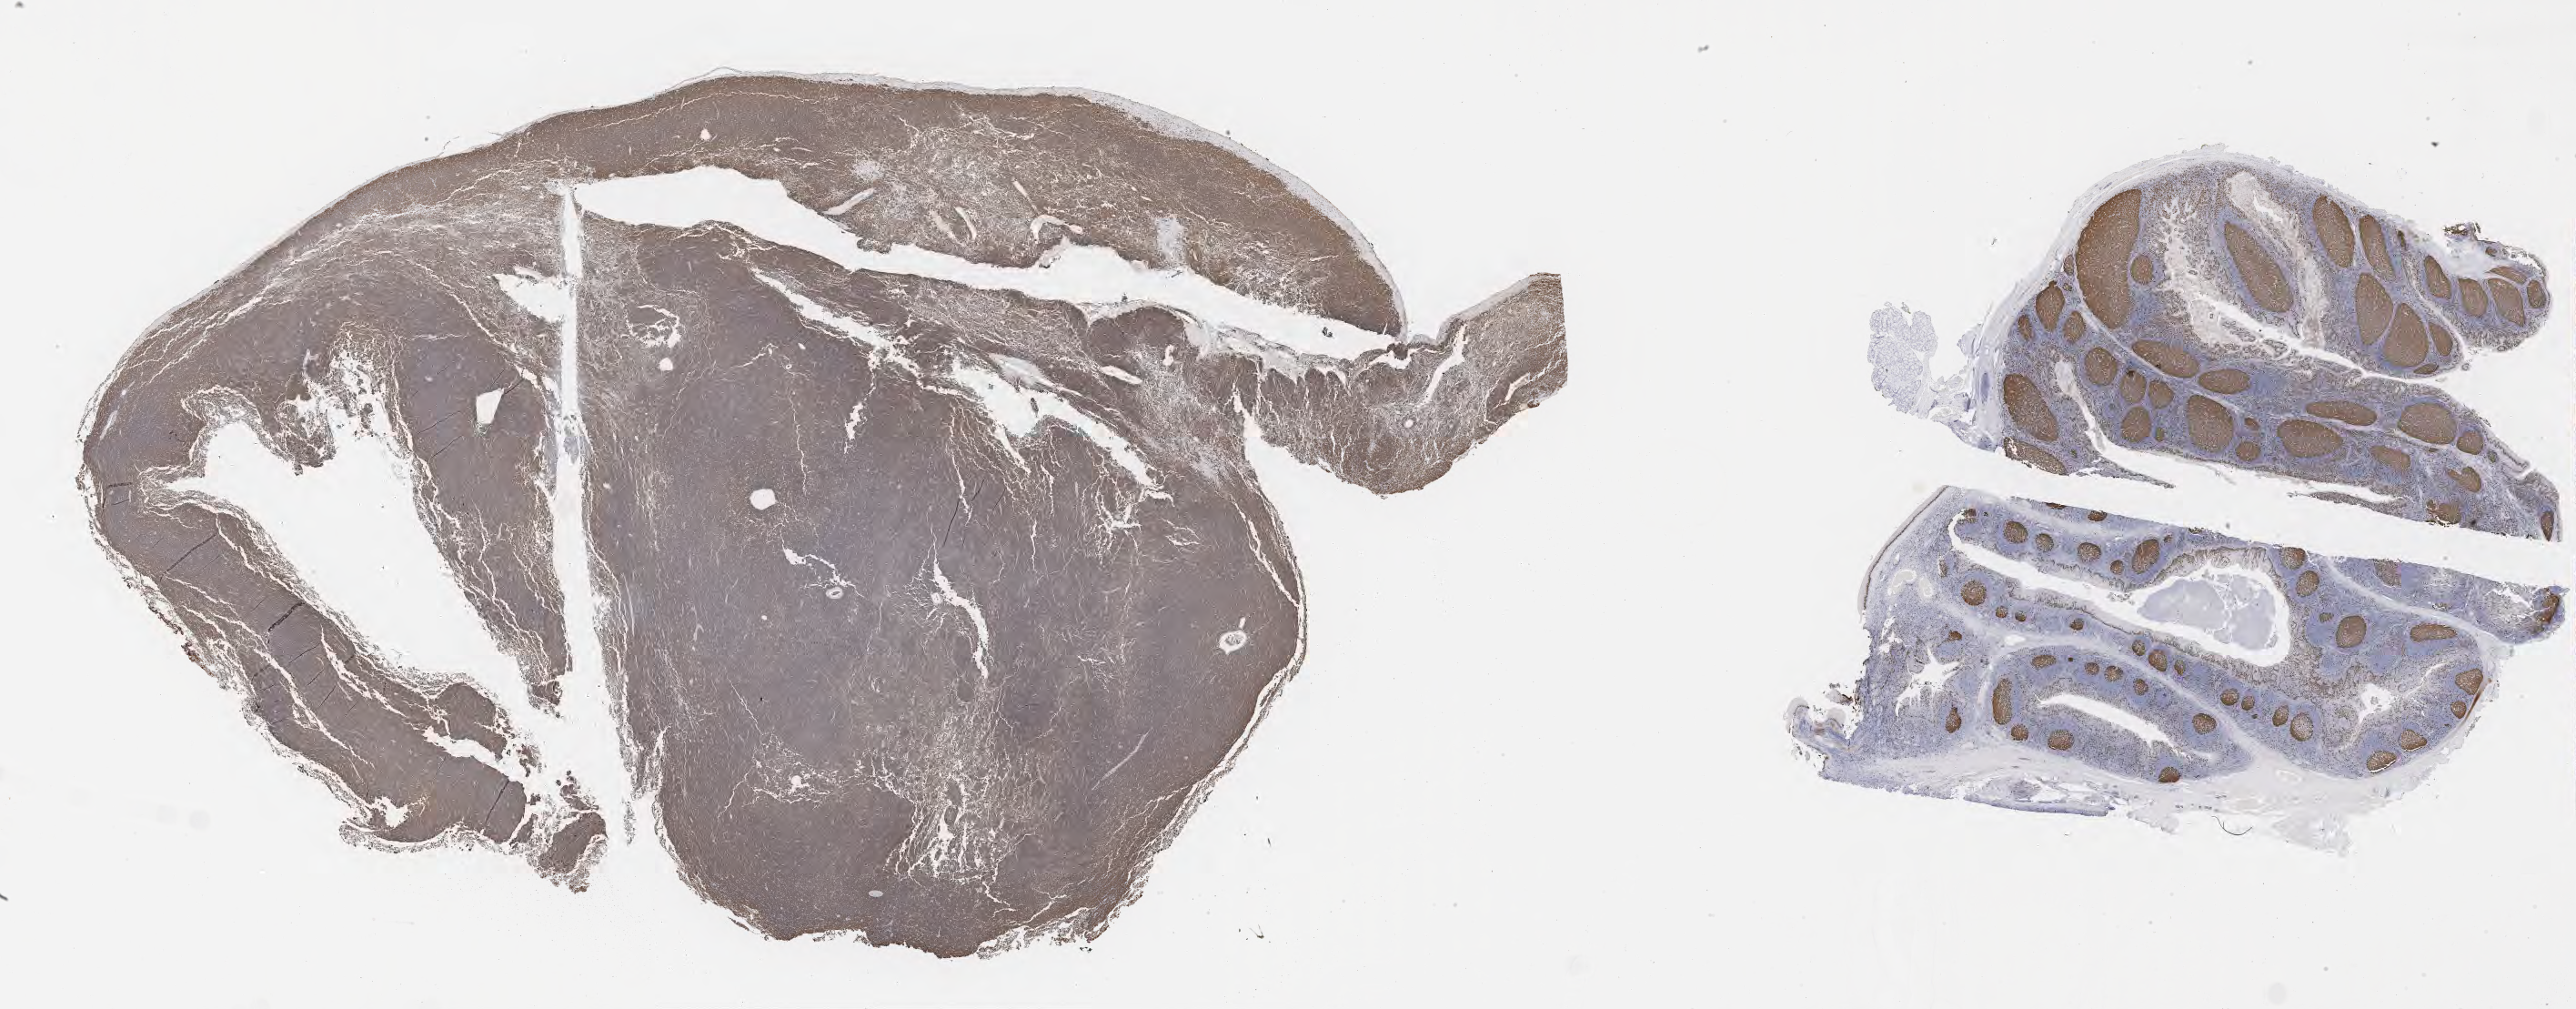
Whole-slide image, immunohistochemical stain for Ki-67 — whole scanned area (about 45.8 x 17.9 mm) shown as a low-resolution overview; tumor tissue. Female, age 3 years at initial diagnosis.
Histologic diagnosis: Burkitt lymphoma, NOS.